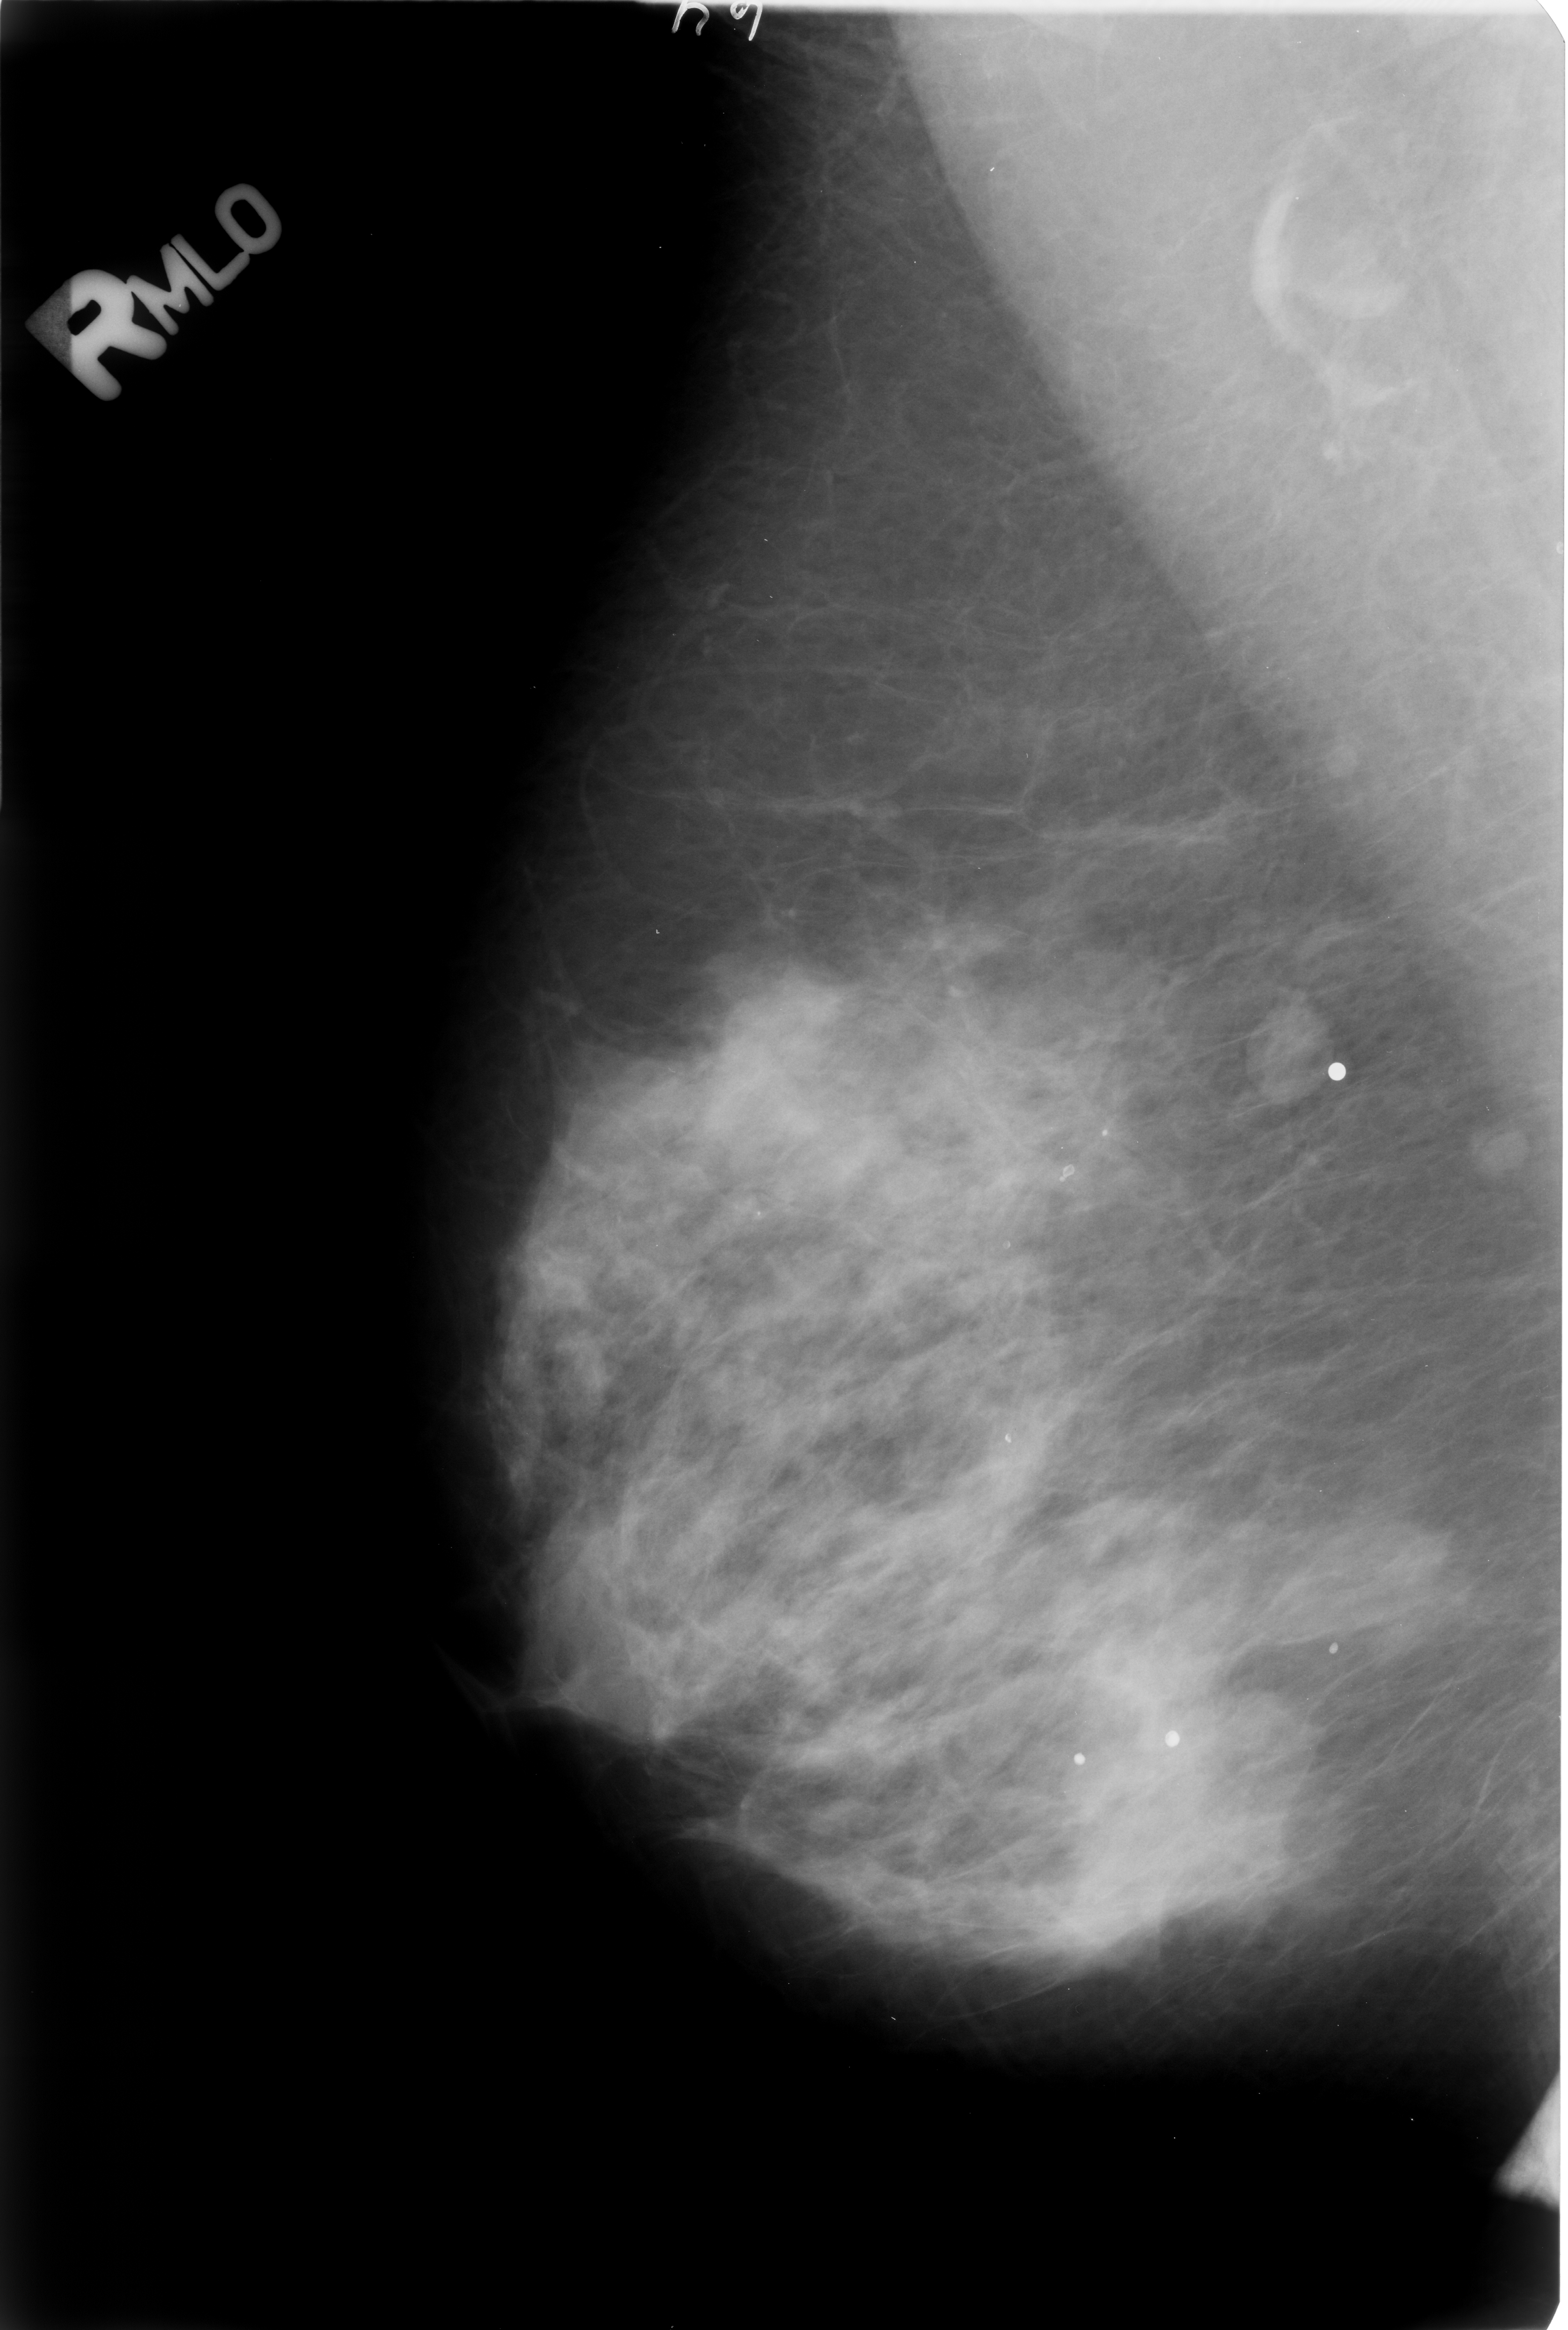
Scanned film-screen mammogram; right breast; MLO view.
Marked findings (only marked abnormalities are described; nothing is implied about the rest of the image): Finding 1 of 4: calcifications, morphology round and regular / lucent center; BI-RADS assessment category 2; subtlety rating 4 on a 1 (subtle) to 5 (obvious) scale; benign; no additional work-up was recommended (benign without callback). Finding 2 of 4: calcifications, morphology round and regular / lucent center; BI-RADS assessment category 2; benign; no additional work-up was recommended (benign without callback). Finding 3 of 4: calcifications, morphology round and regular / lucent center; BI-RADS assessment category 2; subtlety rating 4 on a 1 (subtle) to 5 (obvious) scale; benign without callback (not worked up further). Finding 4 of 4: calcifications, morphology round and regular / lucent center; BI-RADS assessment category 2; subtlety rating 4 on a 1 (subtle) to 5 (obvious) scale; benign without callback (not worked up further).